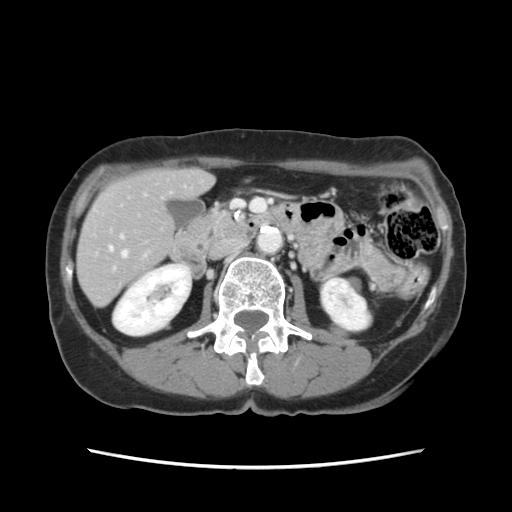
Contrast-enhanced abdominal CT, one axial slice; slice 45 of 120 in the series (ordered by position); intravenous contrast given; soft-tissue window (W 400 / L 40 HU); 512 × 512 image matrix. Female patient, age 70 years. From the clinical record (not read from this slice): diagnosis: colorectal cancer liver metastases, imaged before liver resection.
Outlined on this slice (expert manual segmentation):
- hepatic veins: bounding box [x1, y1, x2, y2] px = [109, 247, 127, 257]
- liver: [78, 170, 212, 304]
- planned liver remnant (the part of the liver to remain after resection): [78, 170, 212, 305]
- portal vein (with intrahepatic branches): [120, 235, 123, 239]